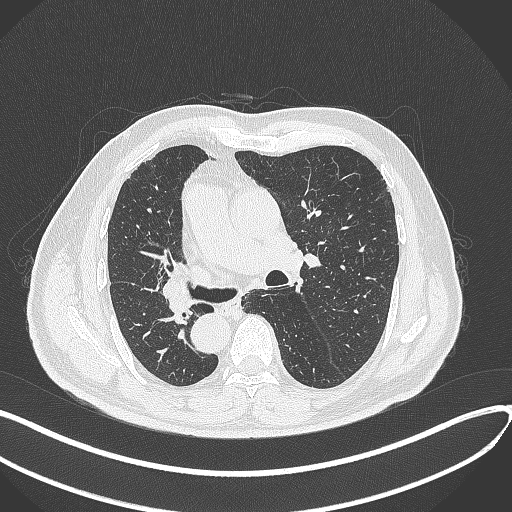
Chest CT, one axial slice. Slice 165 of 300 in the series (ordered by position). Lung window (W 1500 / L -600 HU). 1 mm slice thickness. 512 × 512 image matrix, field of view 400 × 400 mm. Patient: male, 67 years. From the clinical record (not read from this slice): clinical TNM (as recorded): T2a N0 M0.
Structures marked on this image (rectangle marked by the reading radiologist):
- lung tumour (recorded histology: squamous cell carcinoma): box from (x=162, y=282) to (x=198, y=323) px